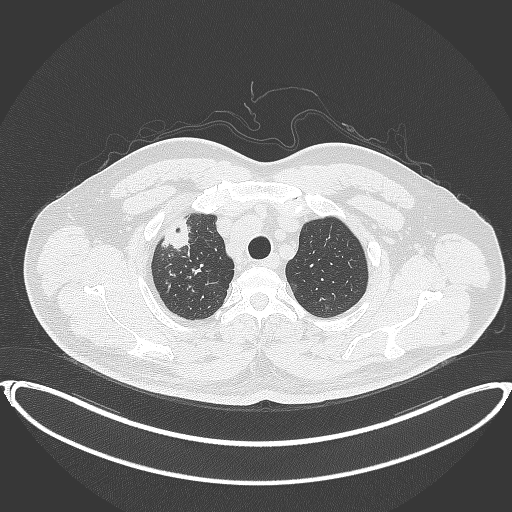
Chest CT, one axial slice; position 335 of 399 along the scan axis; 120 kVp; lung window (W 1500 / L -600 HU); 1 mm slice thickness; 512 × 512 image matrix, field of view 445 × 445 mm. Patient: male, 53 years. From the clinical record (not read from this slice): clinical TNM (as recorded): T2a N0 M0.
Structures marked on this image (rectangle marked by the reading radiologist):
- lung tumour (recorded histology: adenocarcinoma): bounding box (x1, y1, x2, y2) in pixels: (155, 214, 201, 255)